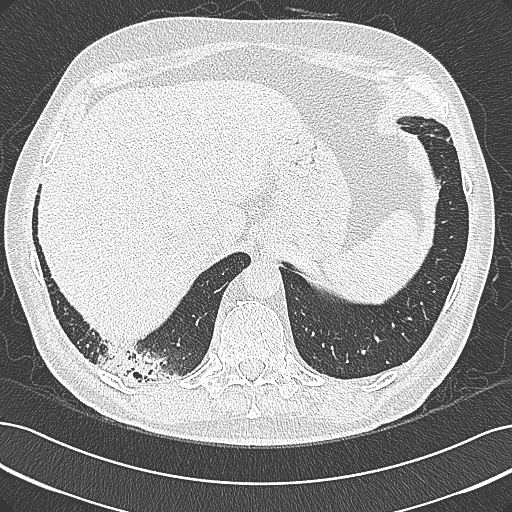
Chest CT (low-dose screening protocol), one axial image; first (baseline) screen; lung window (W 1500 / L -600 HU); 1 mm slice thickness; lung (sharp) reconstruction kernel (B80f). Male, age 68 years at enrolment.
- Expert-annotated lung lesion, bounding box [x1, y1, x2, y2] px = [94, 337, 193, 398].
- Screening reader's record for this exam: no non-calcified nodule ≥4 mm recorded.
- Participant outcome: lung cancer diagnosed 154 days after this screen — mucinous adenocarcinoma, right lower lobe, well differentiated (G1), stage IB (AJCC 6th edition), 50 mm at pathology.